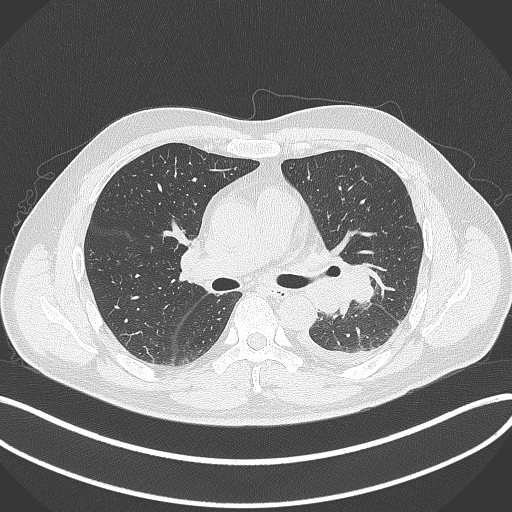
Chest CT, one axial slice; slice 212 of 342 in the series (ordered by position); 120 kVp; lung window (W 1500 / L -600 HU); 1 mm slice thickness; 512 × 512 image matrix, field of view 400 × 400 mm. Male patient, age 58 years. From the clinical record (not read from this slice): clinical TNM (as recorded): T3 N1 M1b; histopathological grade: G3.
Outlined on this slice (rectangle marked by the reading radiologist):
- lung tumour (recorded histology: small cell carcinoma): bounding box <339,257,387,303> (left, top, right, bottom; pixels)